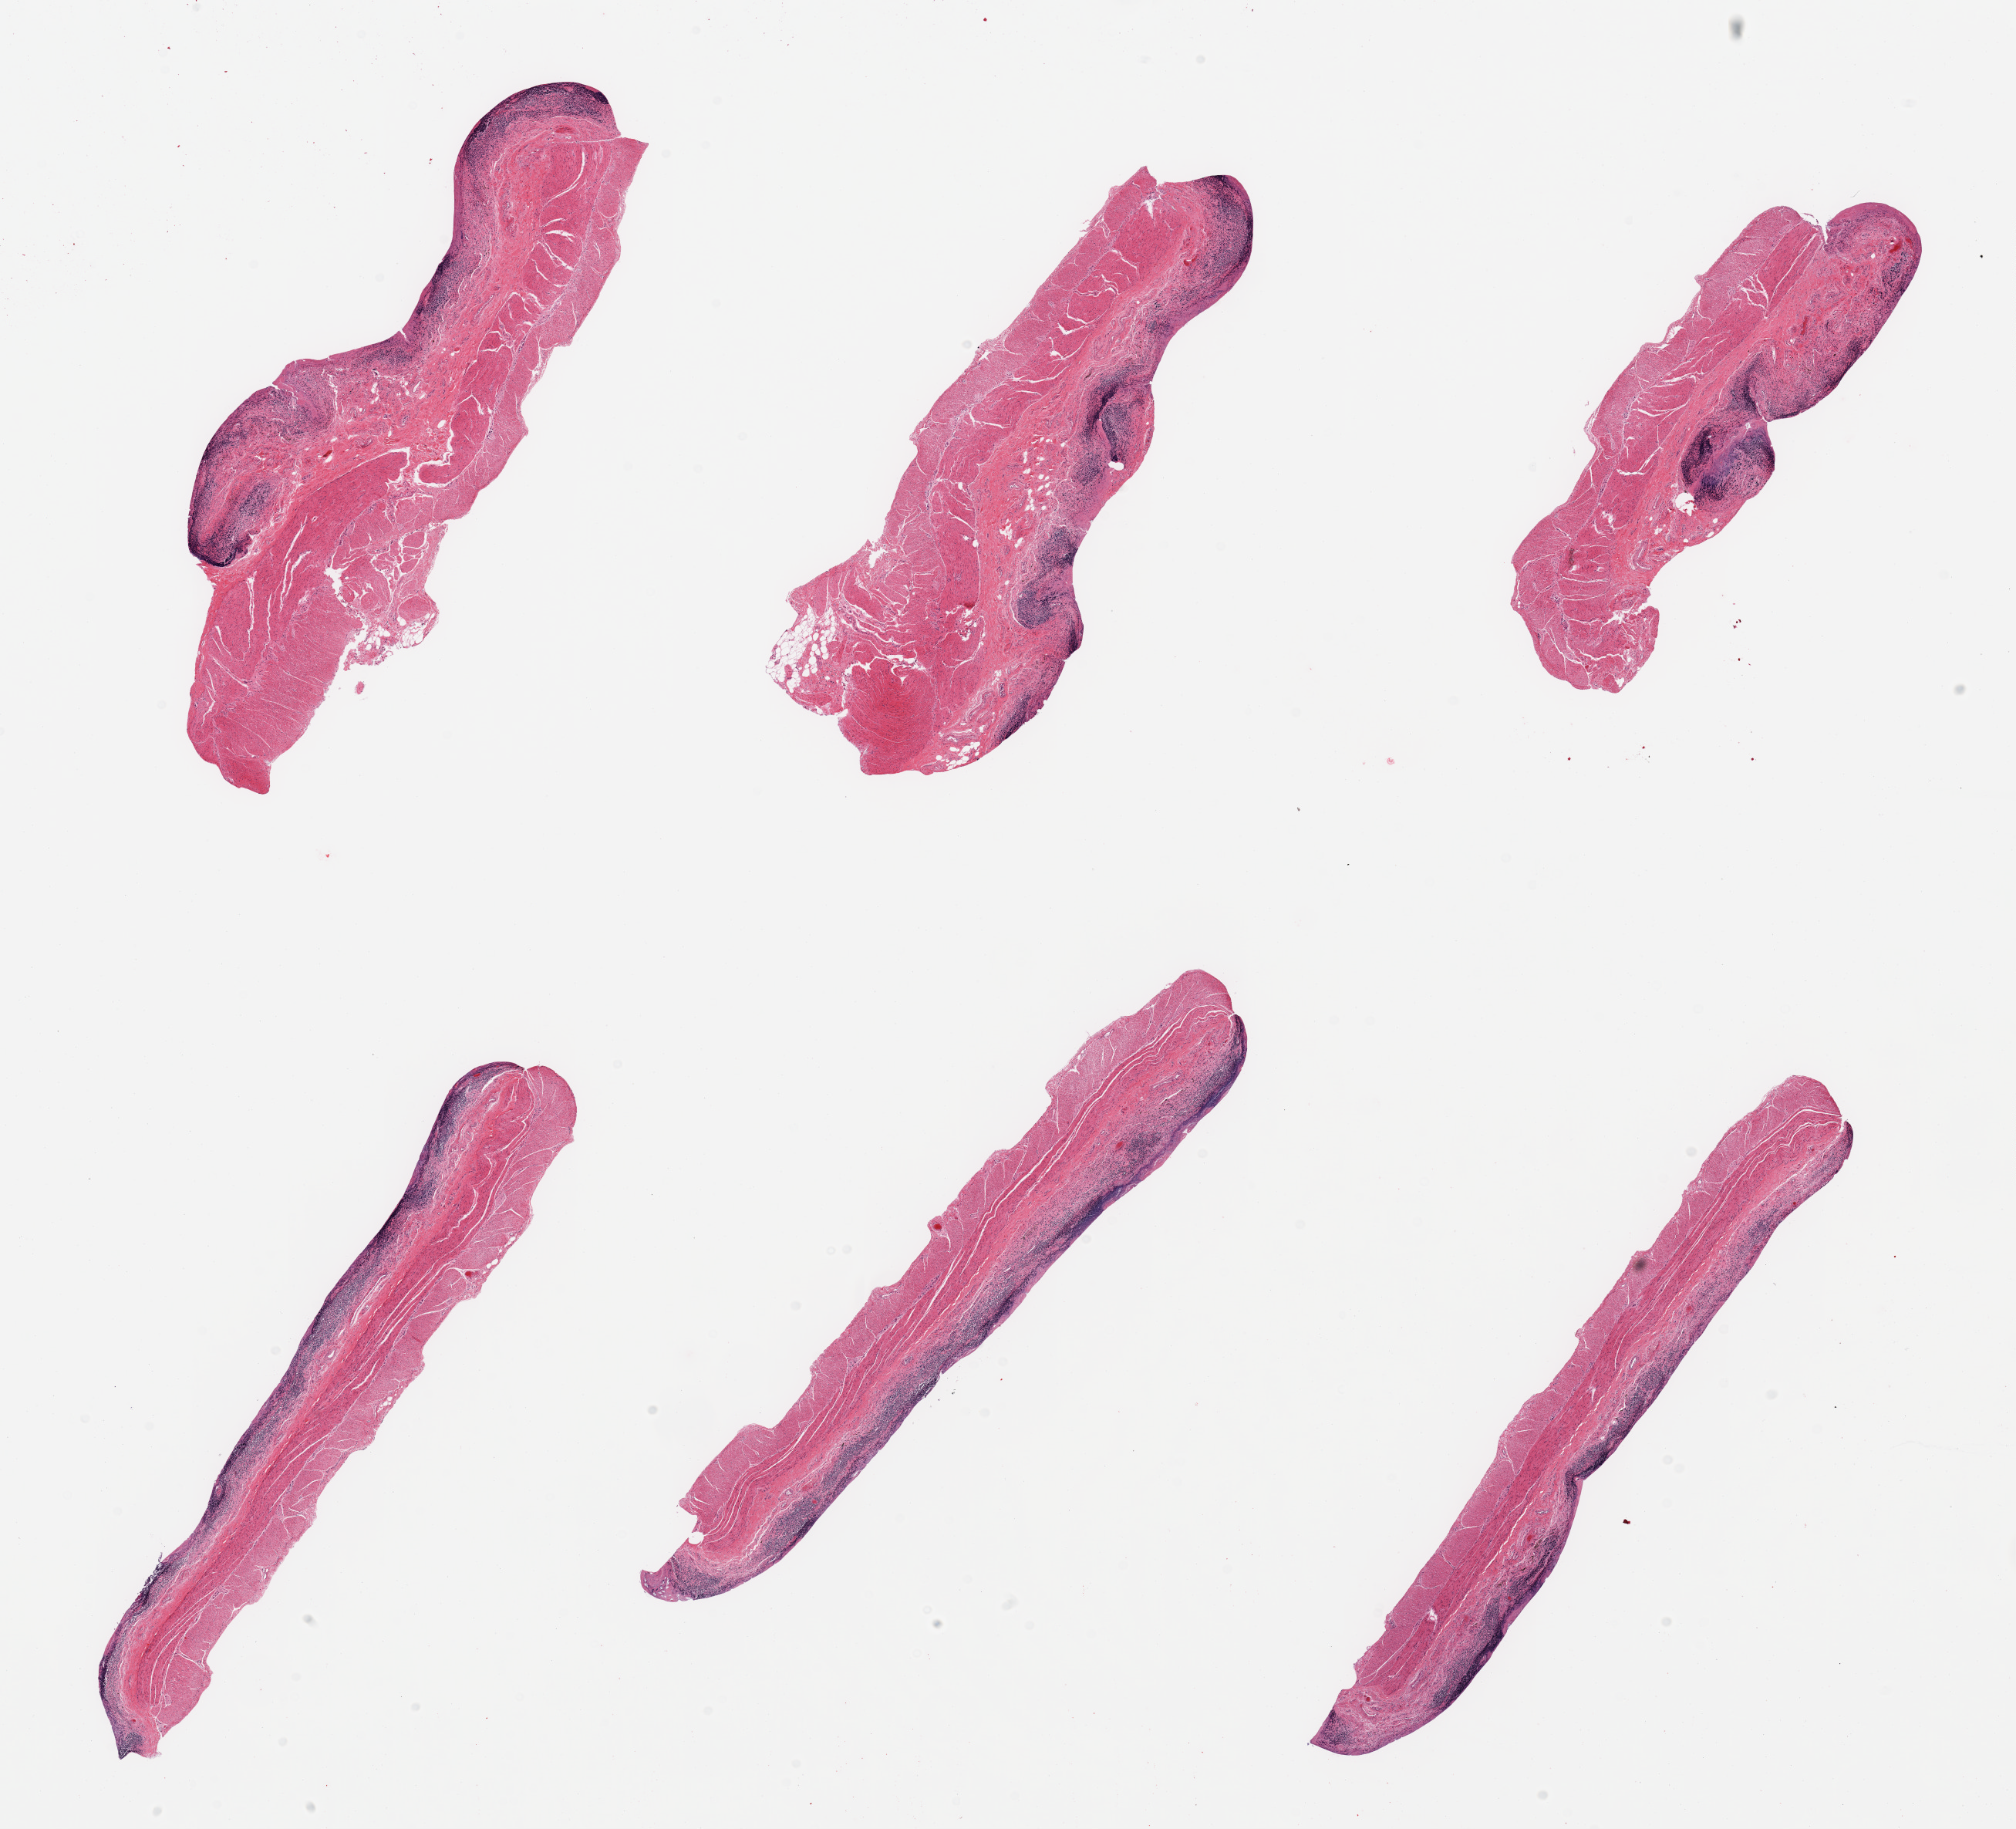
Whole-slide image, haematoxylin and eosin stain, whole scanned area (about 20.7 x 18.8 mm, slide scanned at 20x) shown as a low-resolution overview.
• specimen: PAXgene-fixed, paraffin-embedded tissue; target tissue: ileum; tissue donor sample